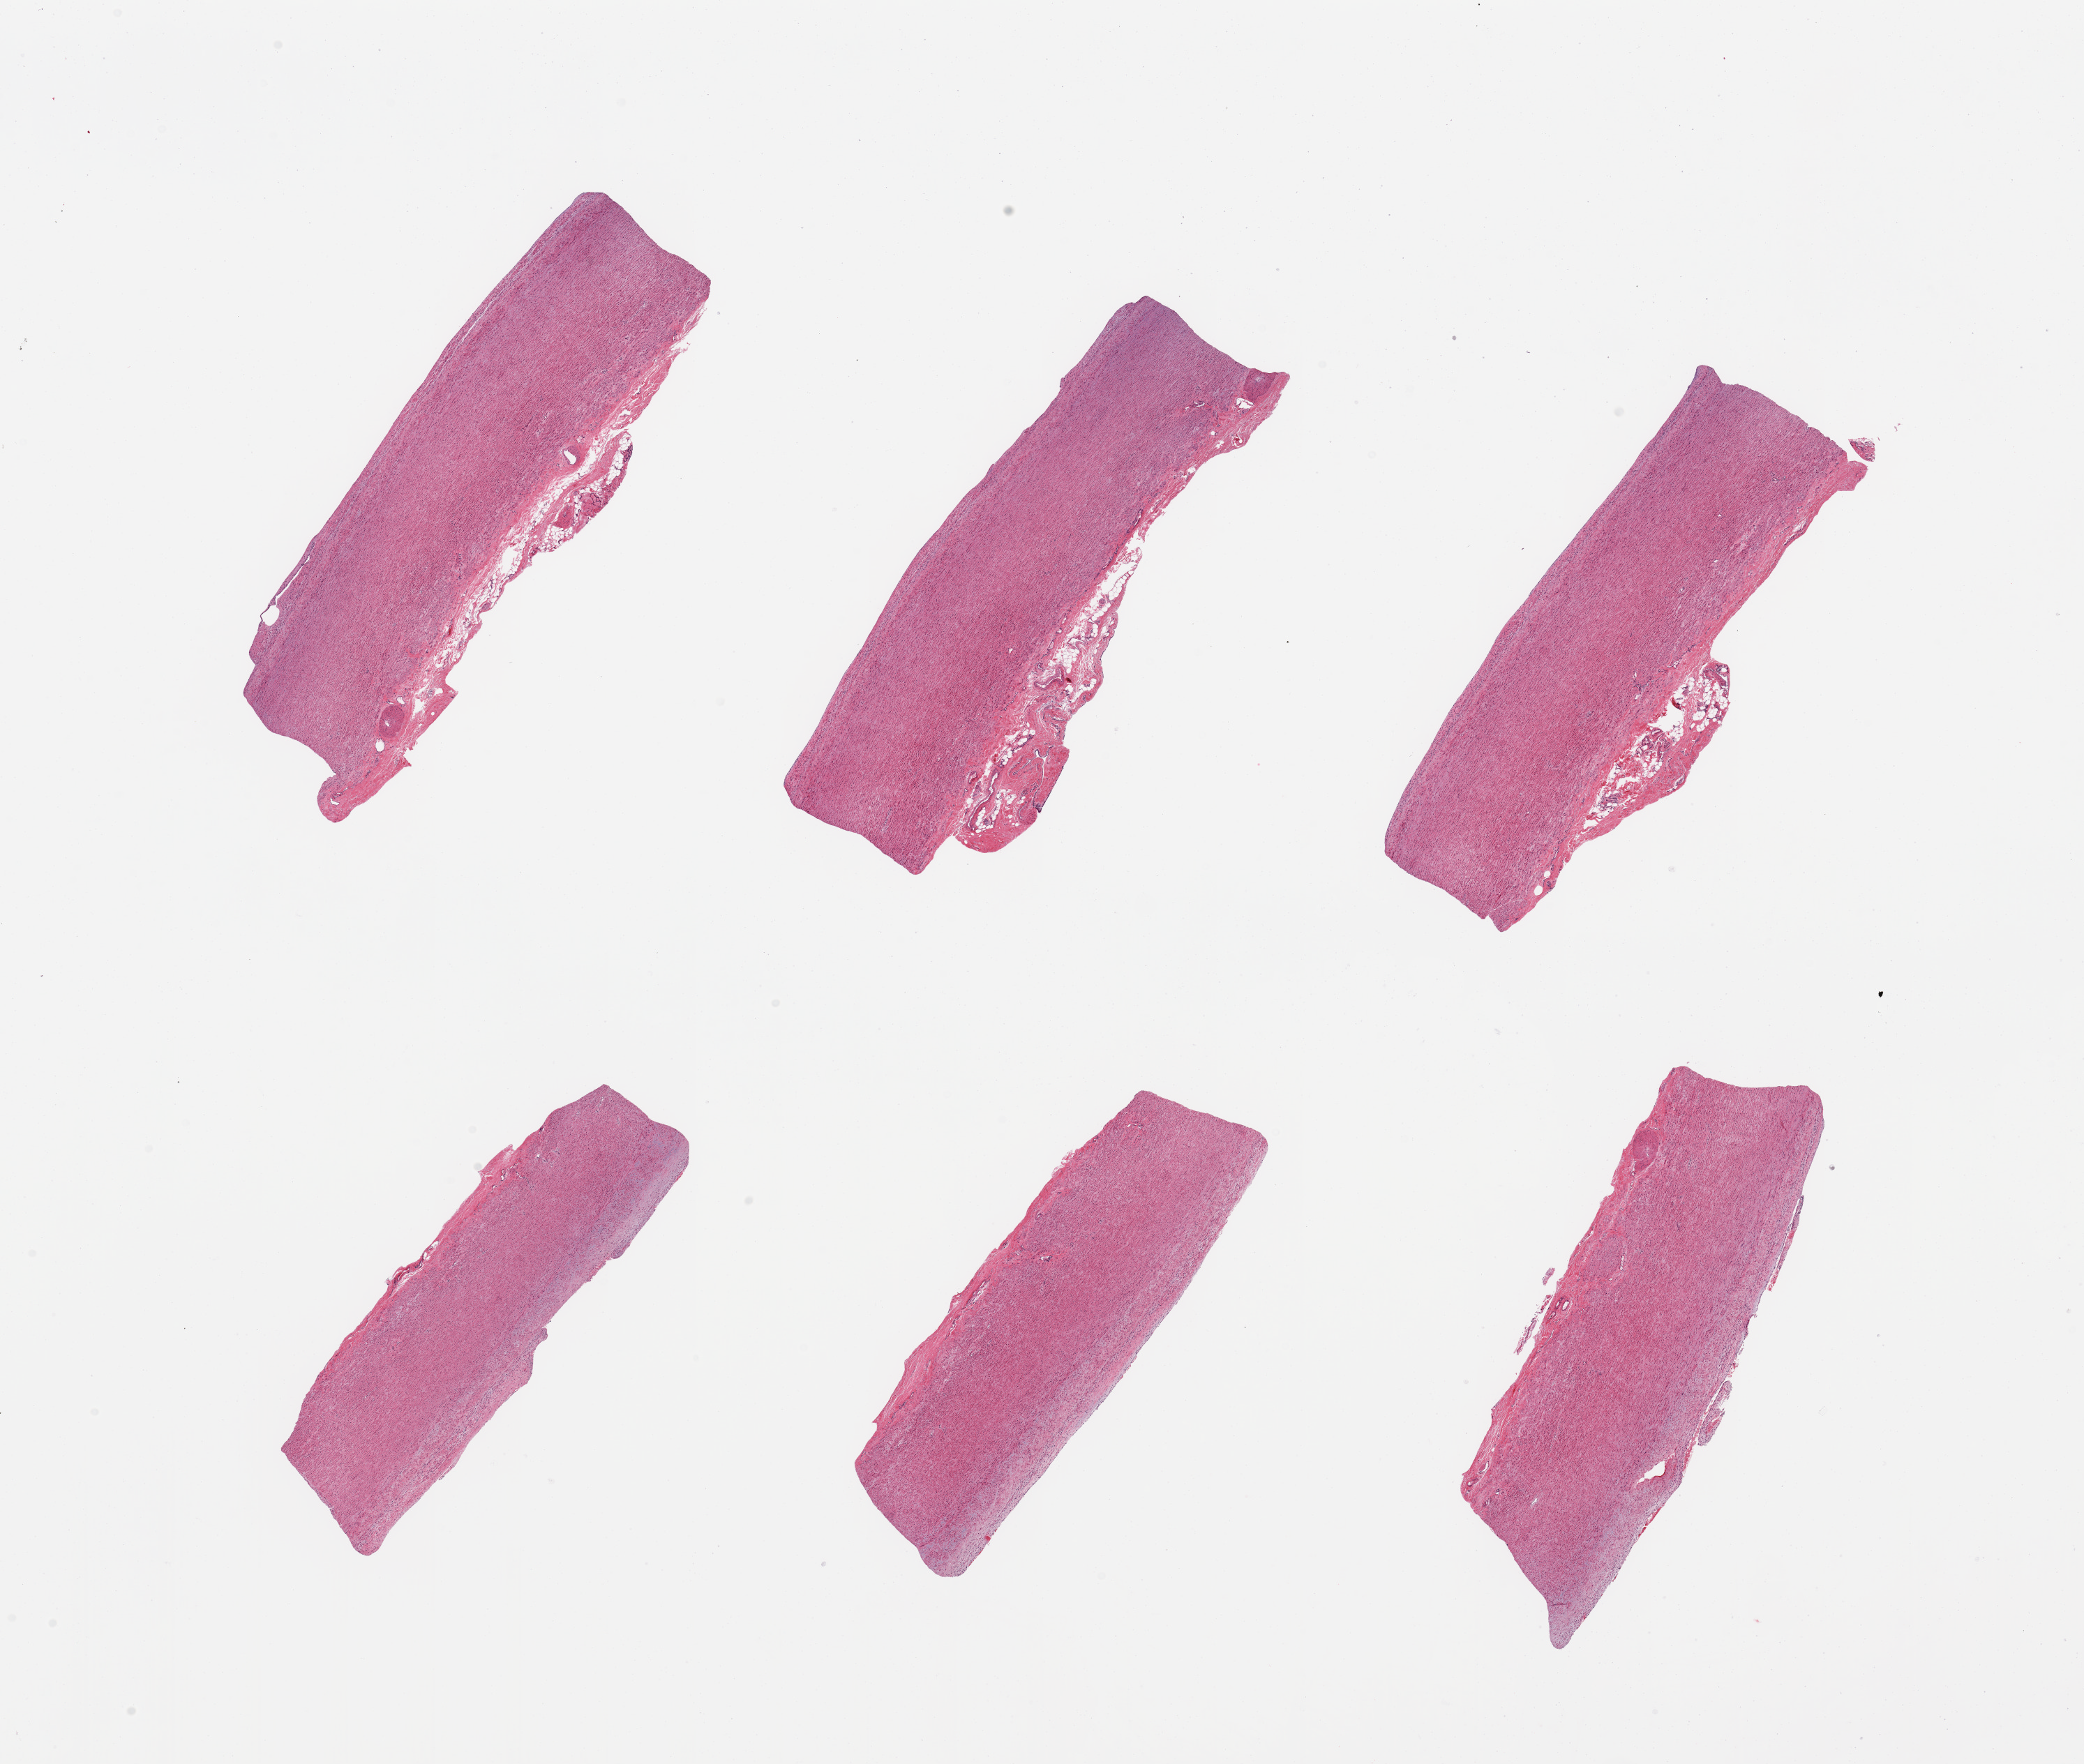
Hematoxylin and eosin (H&E) whole-slide image, brightfield, shown as a low-resolution overview of the whole scanned area (about 23.6 x 20.0 mm); PAXgene-fixed paraffin-embedded (PFPE) section; section of aorta (target tissue); tissue donor sample. Male donor.
Reviewer comment on this tissue sample: 6 pieces; up to 0.75mm attached adventitia.